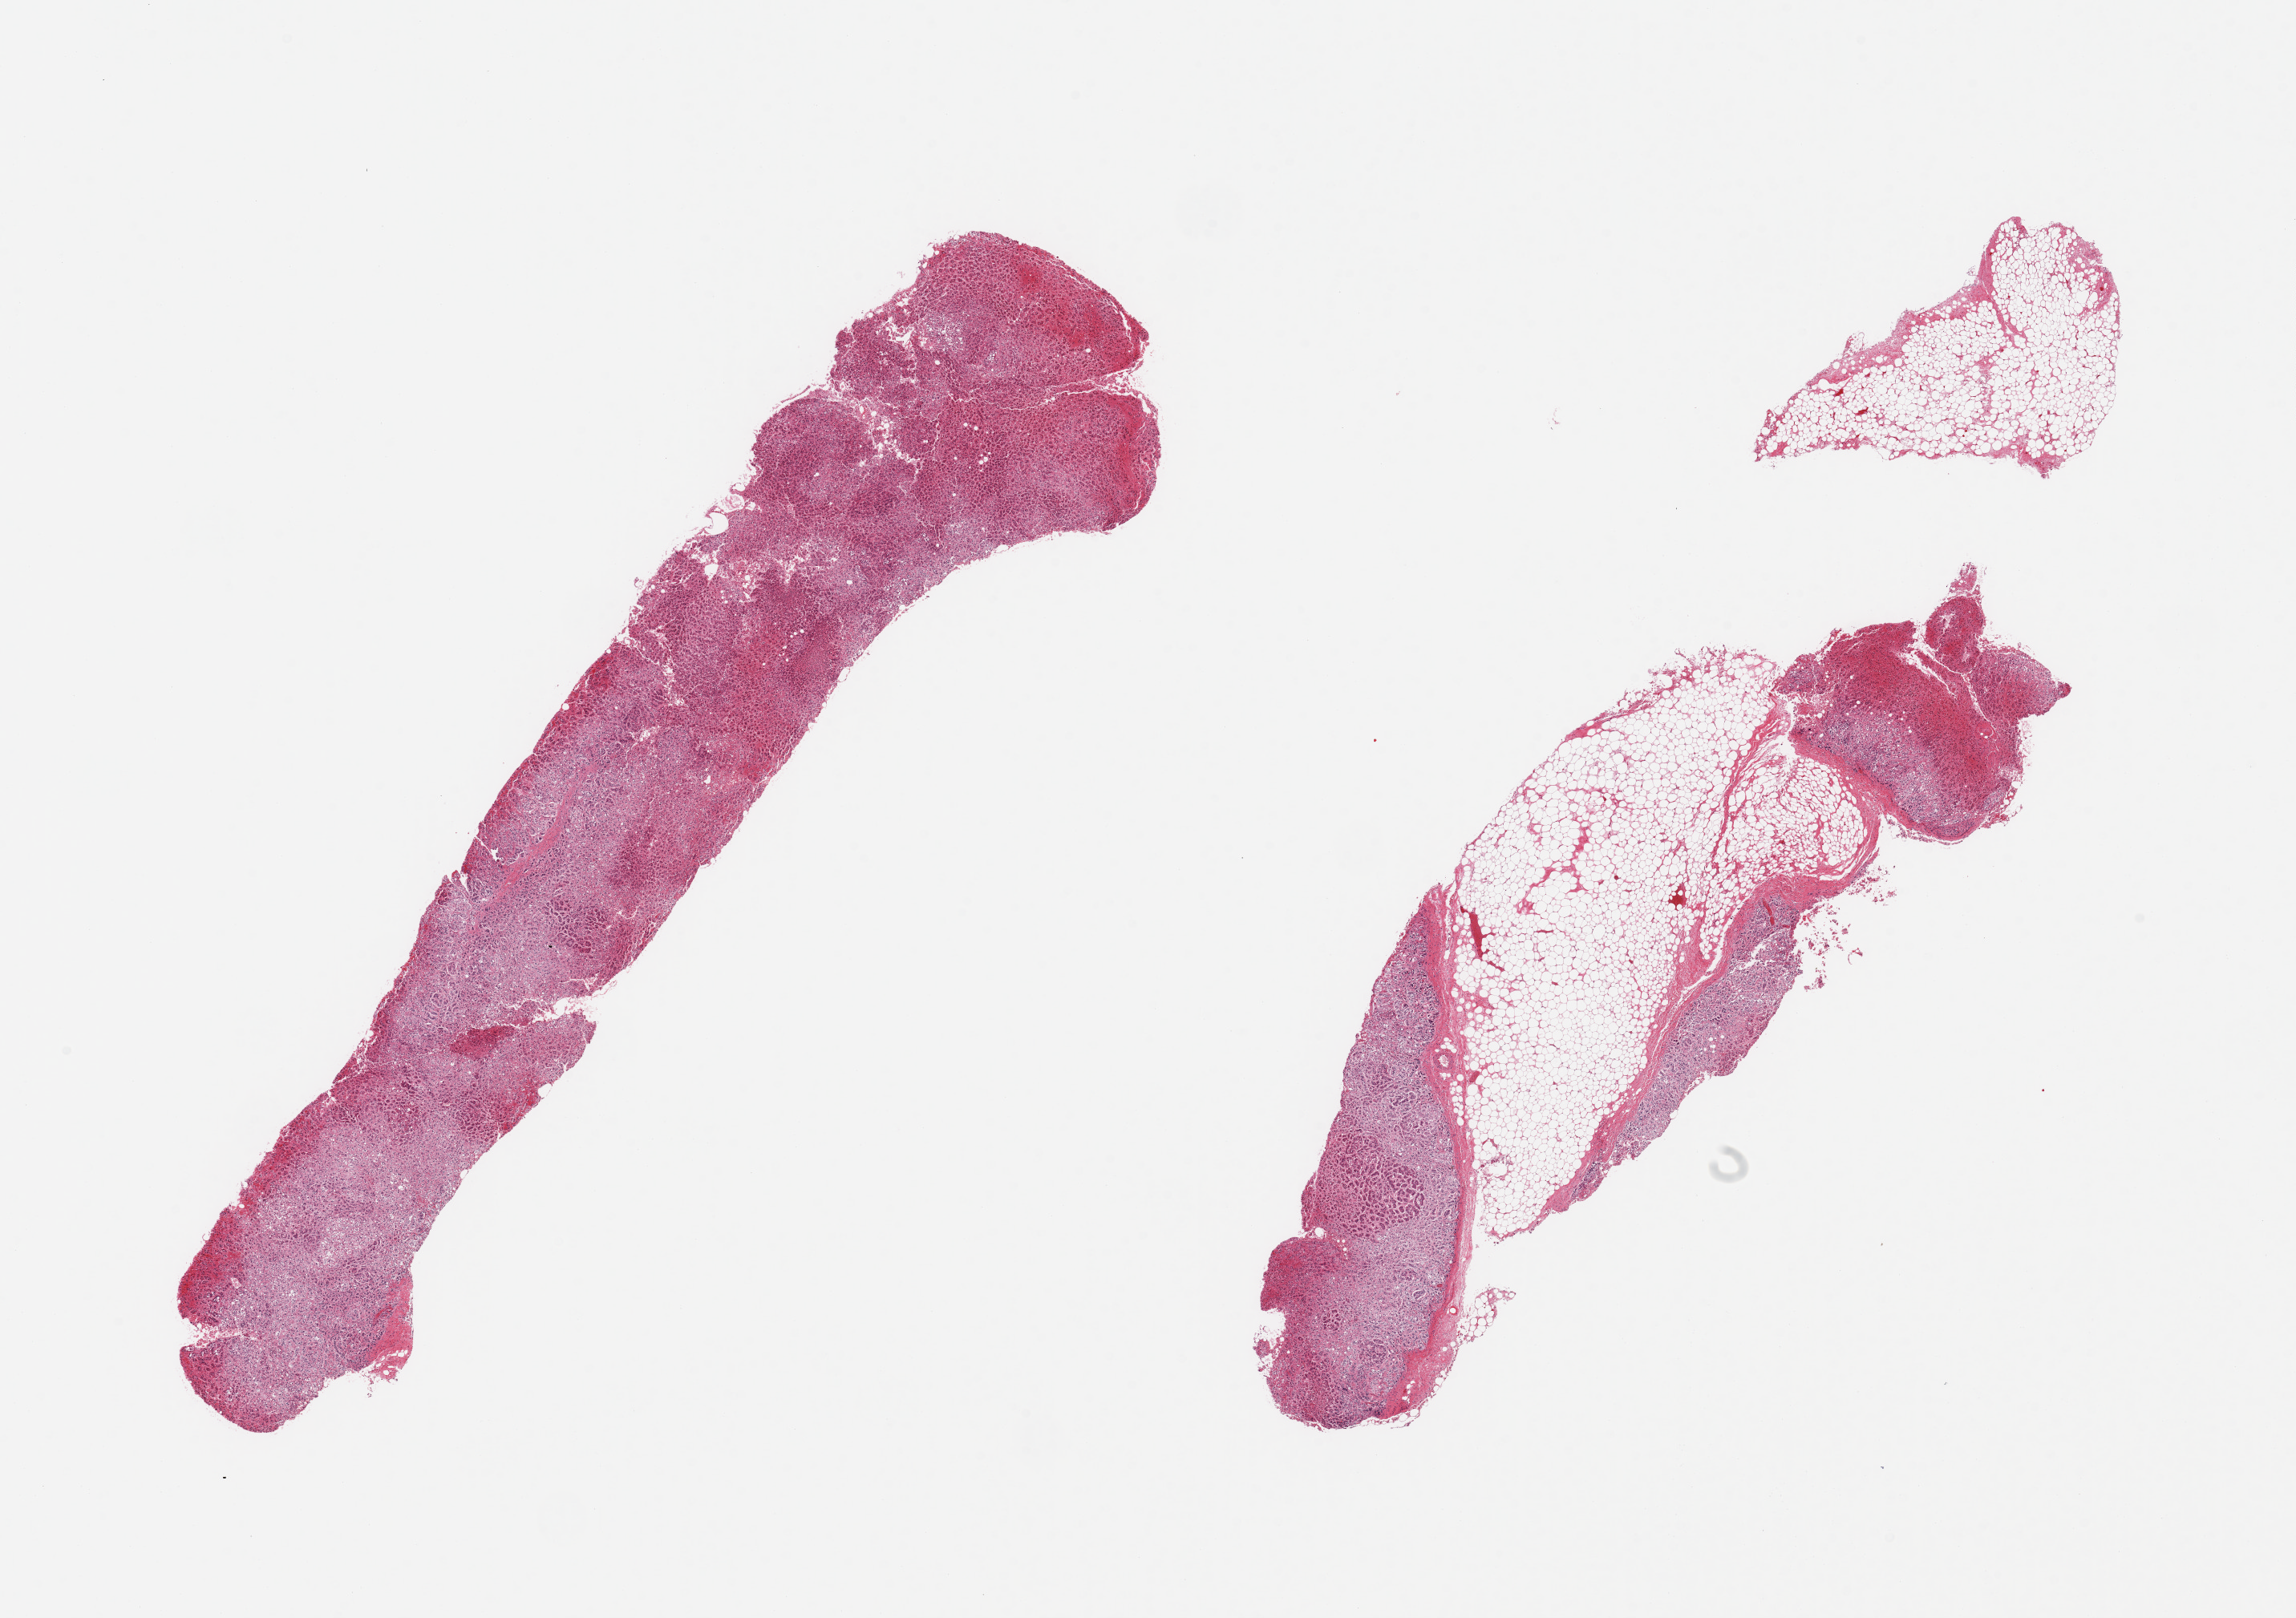
Digitized haematoxylin and eosin-stained section — low-resolution overview of the scanned area, about 22.6 x 16.0 mm (acquisition: 20x scan). PAXgene-fixed paraffin-embedded (PFPE) section. Sampled site (target tissue): adrenal gland. Donor tissue sample.
Reviewer comment on this tissue sample: 2 pieces; 1 piece with 60% fat.